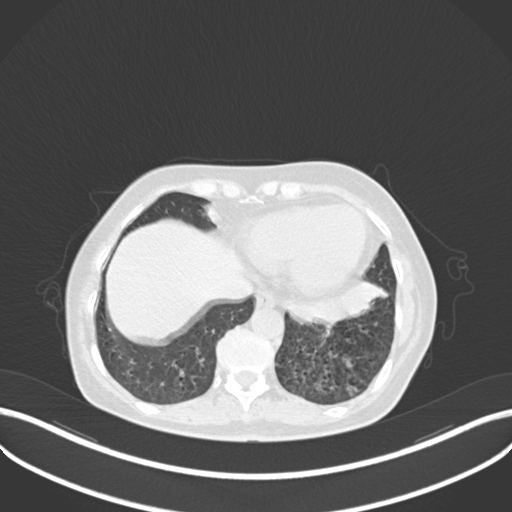
Chest CT, one axial slice. Slice 62 of 270 in the series (ordered by position). 120 kVp. Lung window (W 1500 / L -600 HU). 512 × 512 image matrix, field of view 400 × 400 mm. Female patient, age 63 years. From the clinical record (not read from this slice): clinical TNM (as recorded): T1b N0 M0.
Structures marked on this image (bounding box drawn by a radiologist):
- lung tumour (recorded histology: adenocarcinoma): bounding box [x1, y1, x2, y2] px = [290, 281, 388, 324]